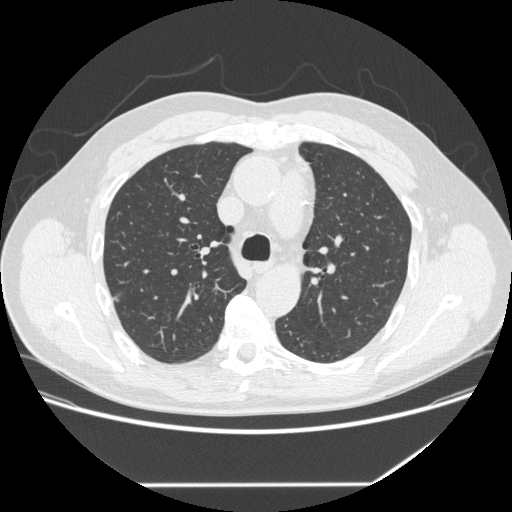
Axial slice from a low-dose chest CT screening exam; baseline screening round; lung window (W 1500 / L -600 HU); 120 kVp; slice 88 of 262 in the series; 512 × 512 image matrix, field of view 400 × 400 mm. Male, age 62 years at enrolment.
Expert reader's lesion annotation, bounding box [x1, y1, x2, y2] px = [101, 279, 131, 315]. Screening reader's record for this exam: no non-calcified nodule ≥4 mm recorded. Lung cancer was diagnosed 839 days after this screen (after the third annual screen): adenocarcinoma, NOS, right upper lobe, moderately differentiated (G2), stage IA (AJCC 6th edition), 12 mm at pathology.